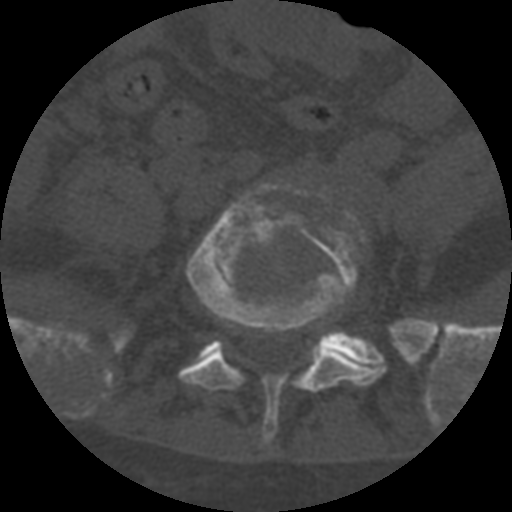
CT including the spine, one axial slice; position 179 of 708 along the scan axis; reconstruction kernel STANDARD; 120 kVp; one of 3 acquisitions stored at this slice position; bone window (W 1800 / L 400 HU); 1.25 mm slice thickness; 512 × 512 image matrix, field of view 160 × 160 mm. Patient age 55 years. Case-level facts recorded for this patient, not image findings: primary cancer: colon; vertebrae with lytic lesions (as recorded): T12, L1, L5.
Outlined on this slice (semi-automatically segmented with operator editing):
- L5 vertebra: bounding box <179,183,386,445> (left, top, right, bottom; pixels)